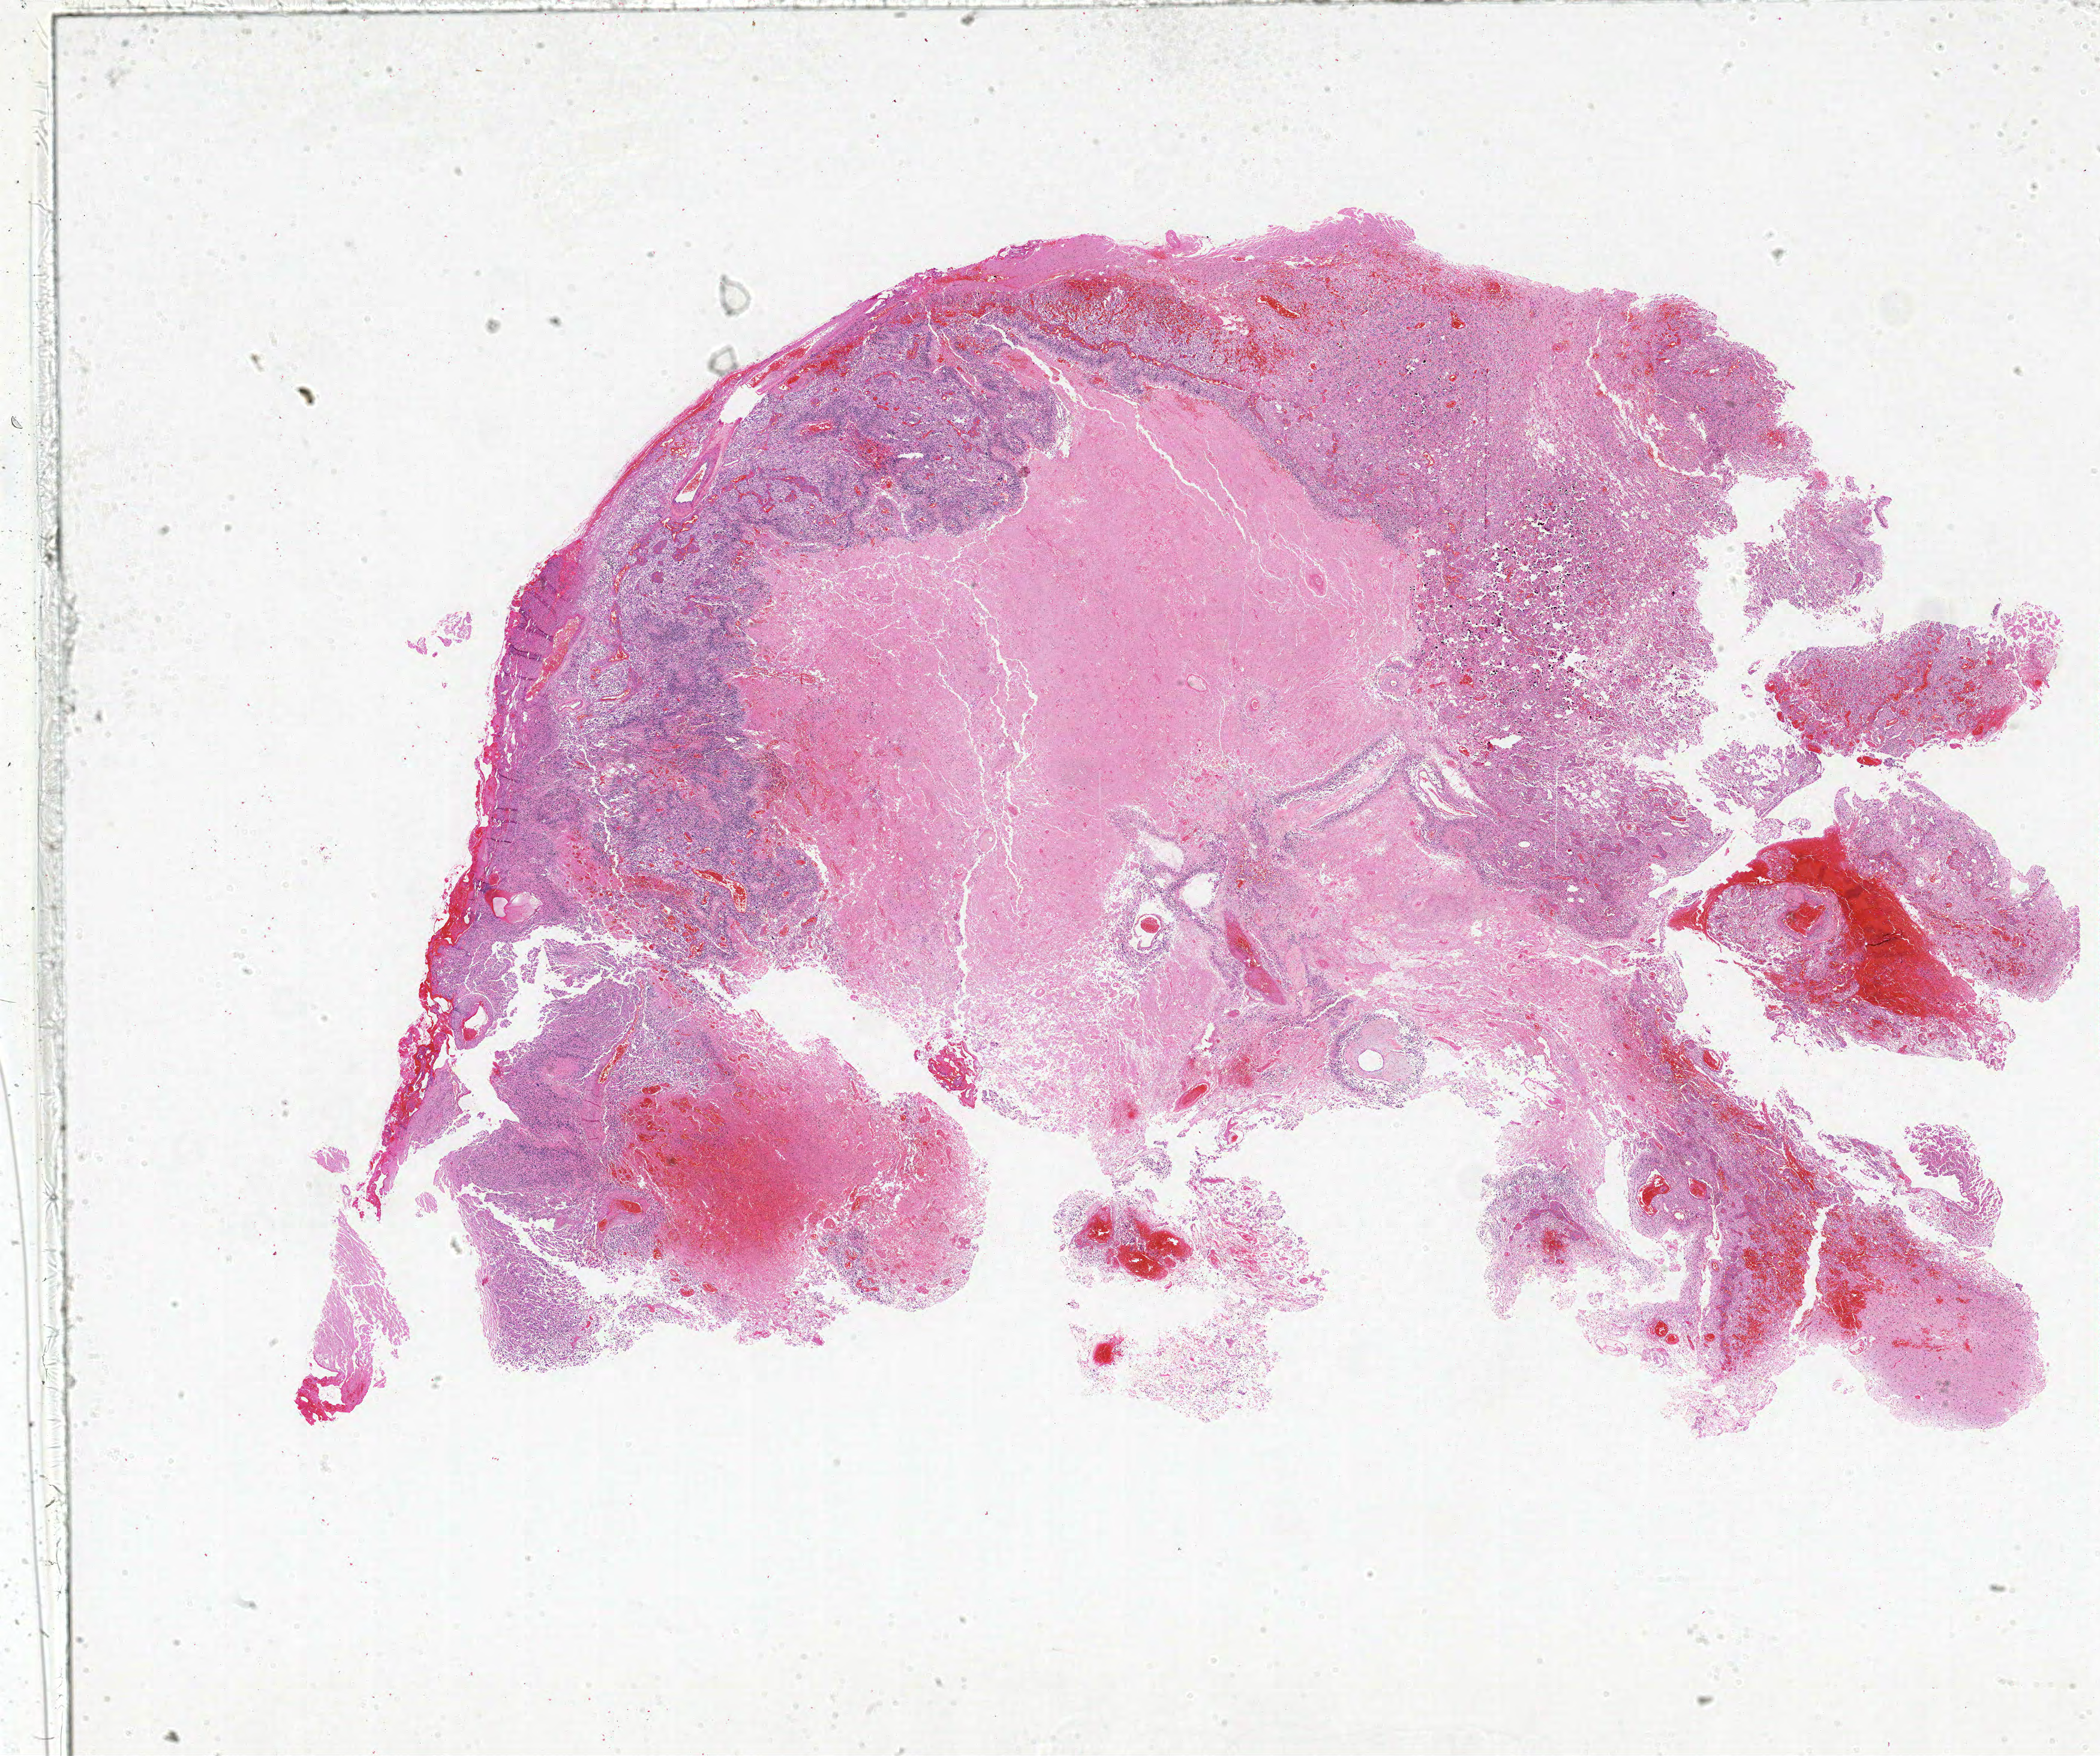
Hematoxylin and eosin (H&E) stained whole-slide image, a low-resolution overview of the entire scanned area, about 28.0 x 23.4 mm (from a 20x scan), formalin-fixed paraffin-embedded (FFPE) diagnostic section, primary tumour sample from the brain. Patient: female, age at initial diagnosis 38 years.
• diagnosis: Glioblastoma